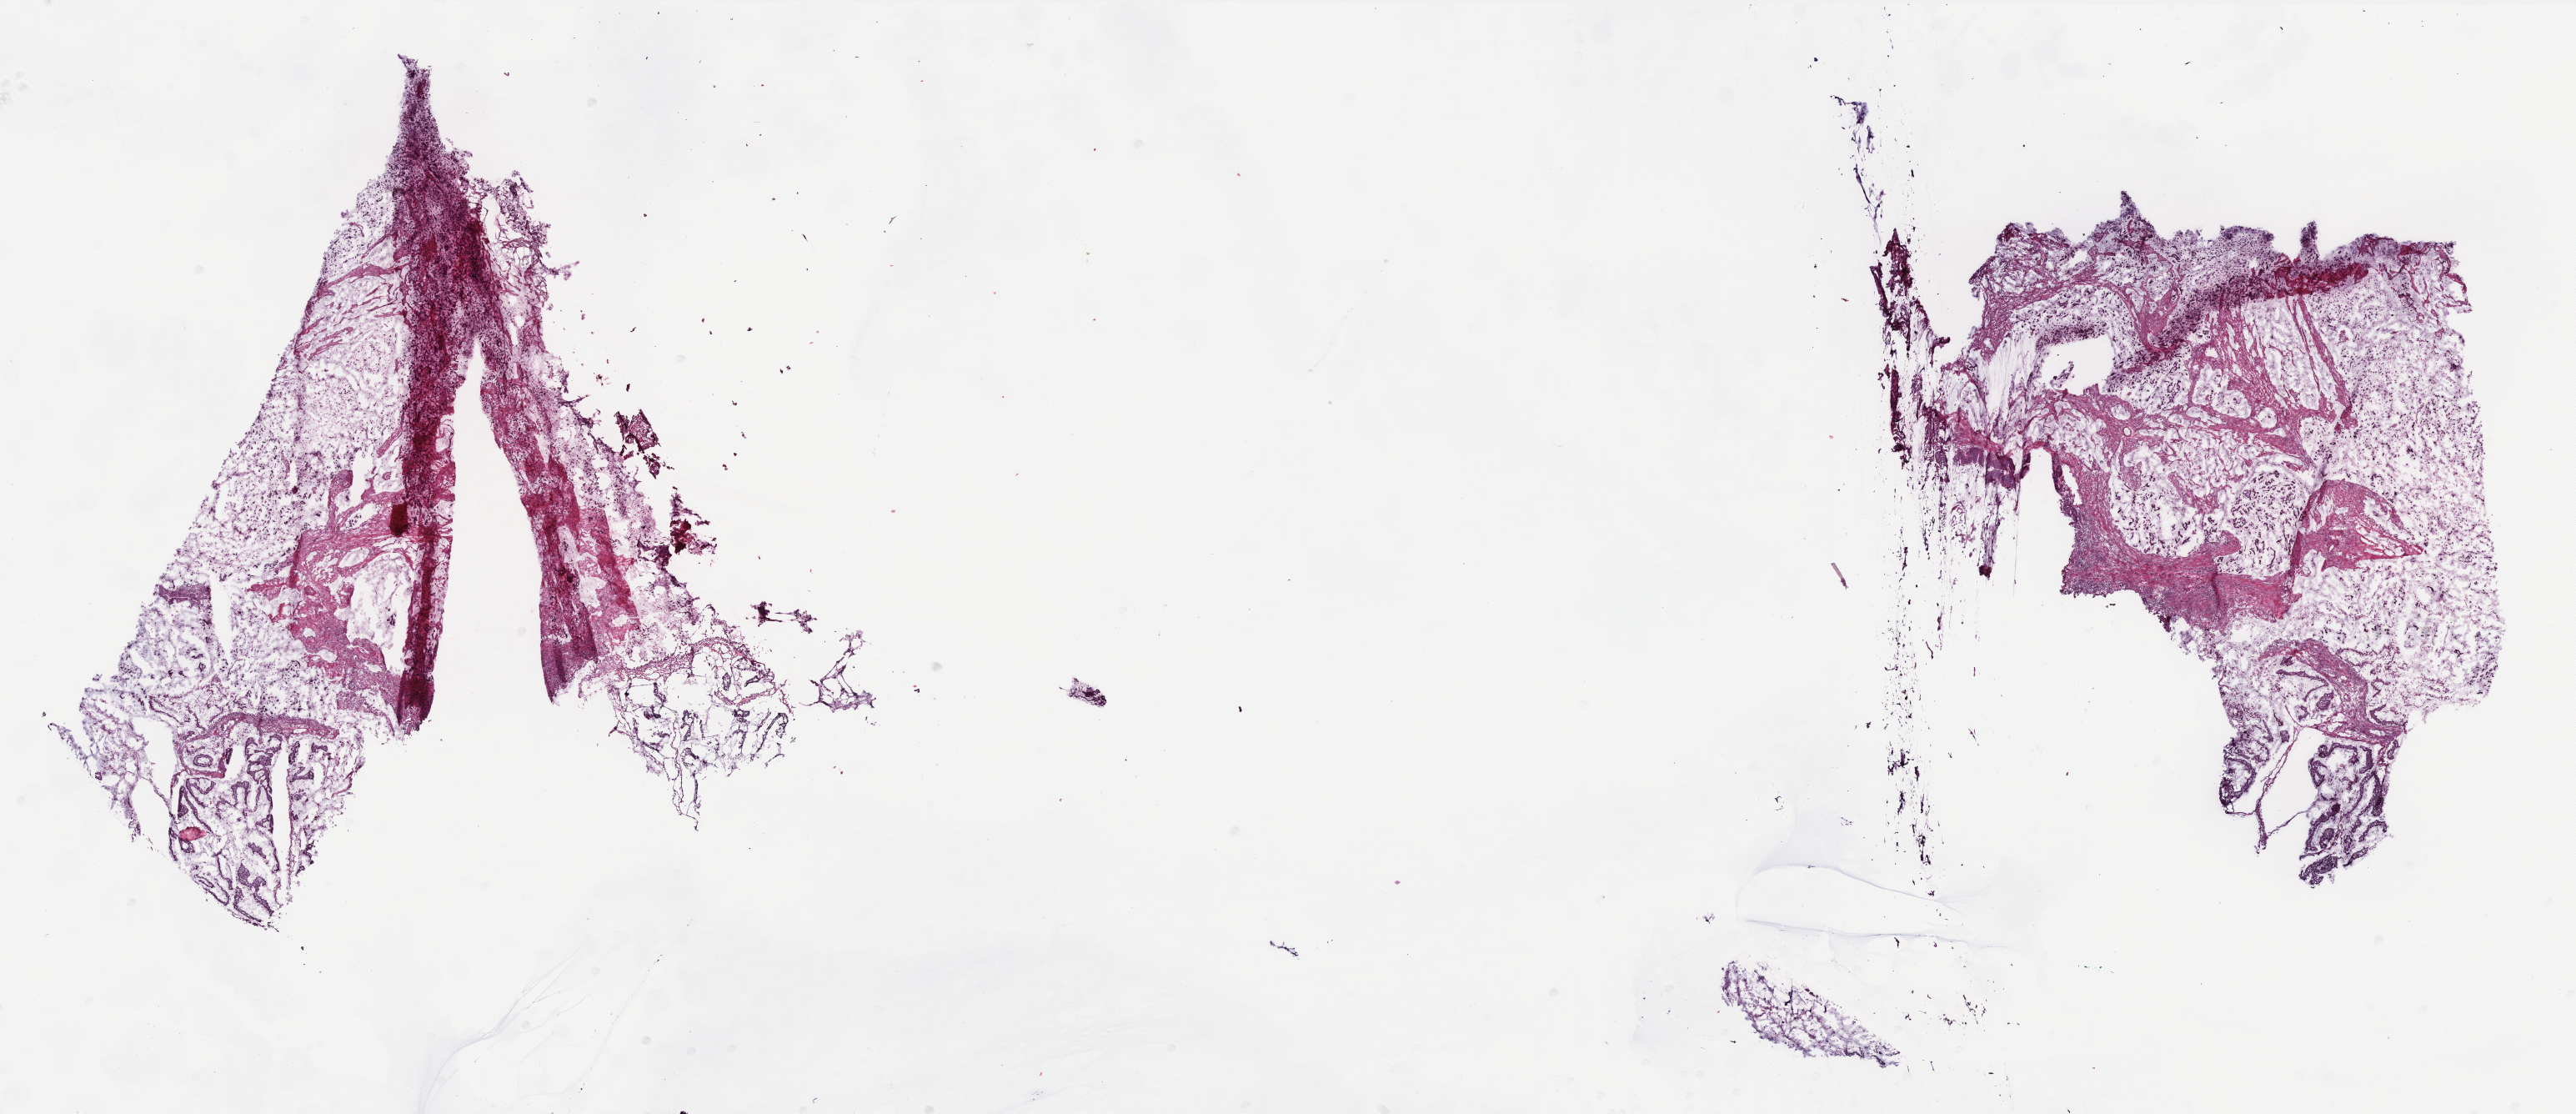
Whole-slide histology image, H&E-stained — low-resolution overview of the scanned area, about 24.8 x 10.7 mm; frozen section; sample: primary tumour, colon. Male, age 75 years at initial diagnosis. Composition of this section per pathologist review: tumour cells 45%, tumour nuclei 70%, normal cells 0%, stromal cells 45%, necrosis 10%. Inflammatory infiltration, as recorded: lymphocyte infiltration 12%, monocyte infiltration 1%, neutrophil infiltration 4%.
AJCC pathologic stage: IIB. TNM: T4 N0 M0. Histologic diagnosis: Mucinous adenocarcinoma. Lymph nodes positive (case pathology): 0 of 21 examined.